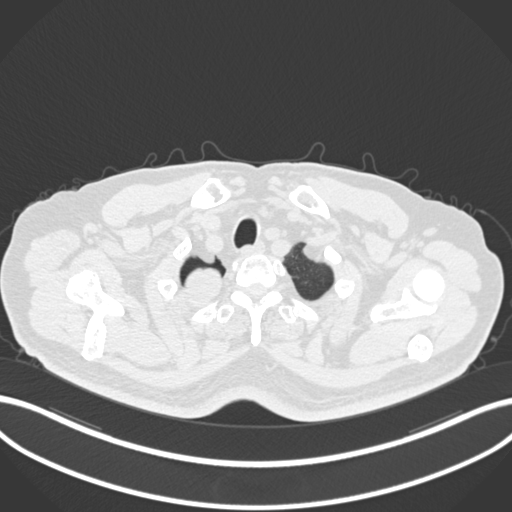
Chest CT, one axial slice. Position 201 of 218 along the scan axis. Reconstruction kernel B30f. 120 kVp. Lung window (W 1500 / L -600 HU). 1 mm slice thickness. 512 × 512 image matrix, field of view 400 × 400 mm. Patient: male, 68 years. Case-level facts recorded for this patient, not image findings: clinical TNM (as recorded): T2a N0 M0.
Structures marked on this image (bounding box drawn by a radiologist):
- lung tumour (recorded histology: adenocarcinoma): bounding box (x1, y1, x2, y2) in pixels: (182, 259, 223, 303)